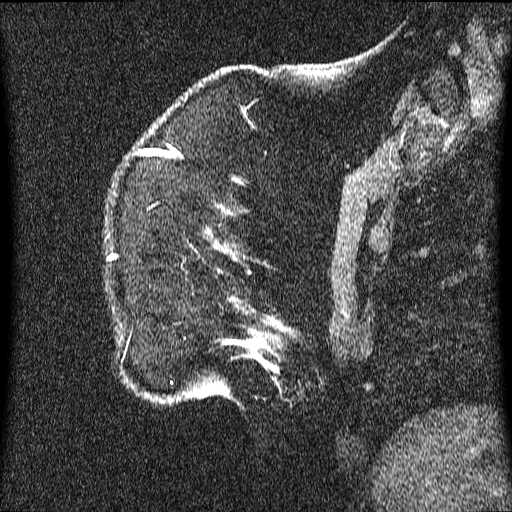
Breast MRI (dynamic contrast-enhanced), one sagittal slice. Dynamic contrast-enhanced series, image 2 of 3 at this slice position (ordered by acquisition). 1.5 T. TE 4.2 ms, TR 9.1 ms. 512 × 512 image matrix, field of view 180 × 180 mm. Patient: female, 52 years.
Outlined on this slice (semi-automatically segmented with operator editing):
- analysis volume of interest (the breast-tissue region the enhancement analysis was run in; not a lesion): bounding box <106,209,344,403> (left, top, right, bottom; pixels)
- tumour enhancement mask (voxels above the 70 % enhancement threshold inside the analysis volume of interest): <226,341,262,362>